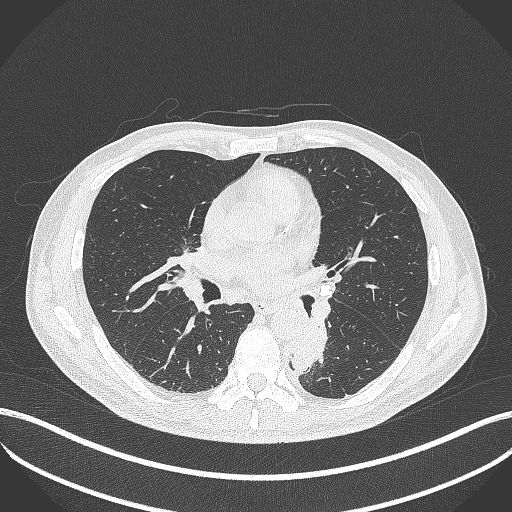
Chest CT, one axial slice; slice 215 of 451 in the series (ordered by position); 120 kVp; lung window (W 1500 / L -600 HU); 1 mm slice thickness; 512 × 512 image matrix, field of view 400 × 400 mm. Patient: male, 72 years. From the clinical record (not read from this slice): clinical TNM (as recorded): T2b N0 M1.
Annotated regions visible in this slice (bounding box drawn by a radiologist):
- lung tumour (recorded histology: adenocarcinoma): bounding box (x1, y1, x2, y2) in pixels: (289, 316, 335, 374)